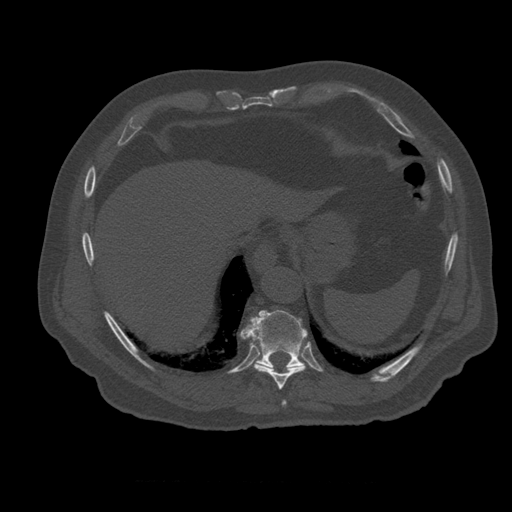
CT including the spine, one axial slice; position 311 of 399 along the scan axis; reconstruction kernel STANDARD; bone window (W 1800 / L 400 HU); 512 × 512 image matrix, field of view 407 × 407 mm. Patient age 73 years. From the clinical record (not read from this slice): primary cancer: prostate; vertebrae with lytic lesions (as recorded): L2.
Structures marked on this image (semi-automatic segmentation, software-assisted and operator-edited):
- T10 vertebra: bounding box <240,310,308,369> (left, top, right, bottom; pixels)
- T12 vertebra: <267,346,280,360>
- T8 vertebra: <283,401,287,406>
- T9 vertebra: <254,347,306,390>